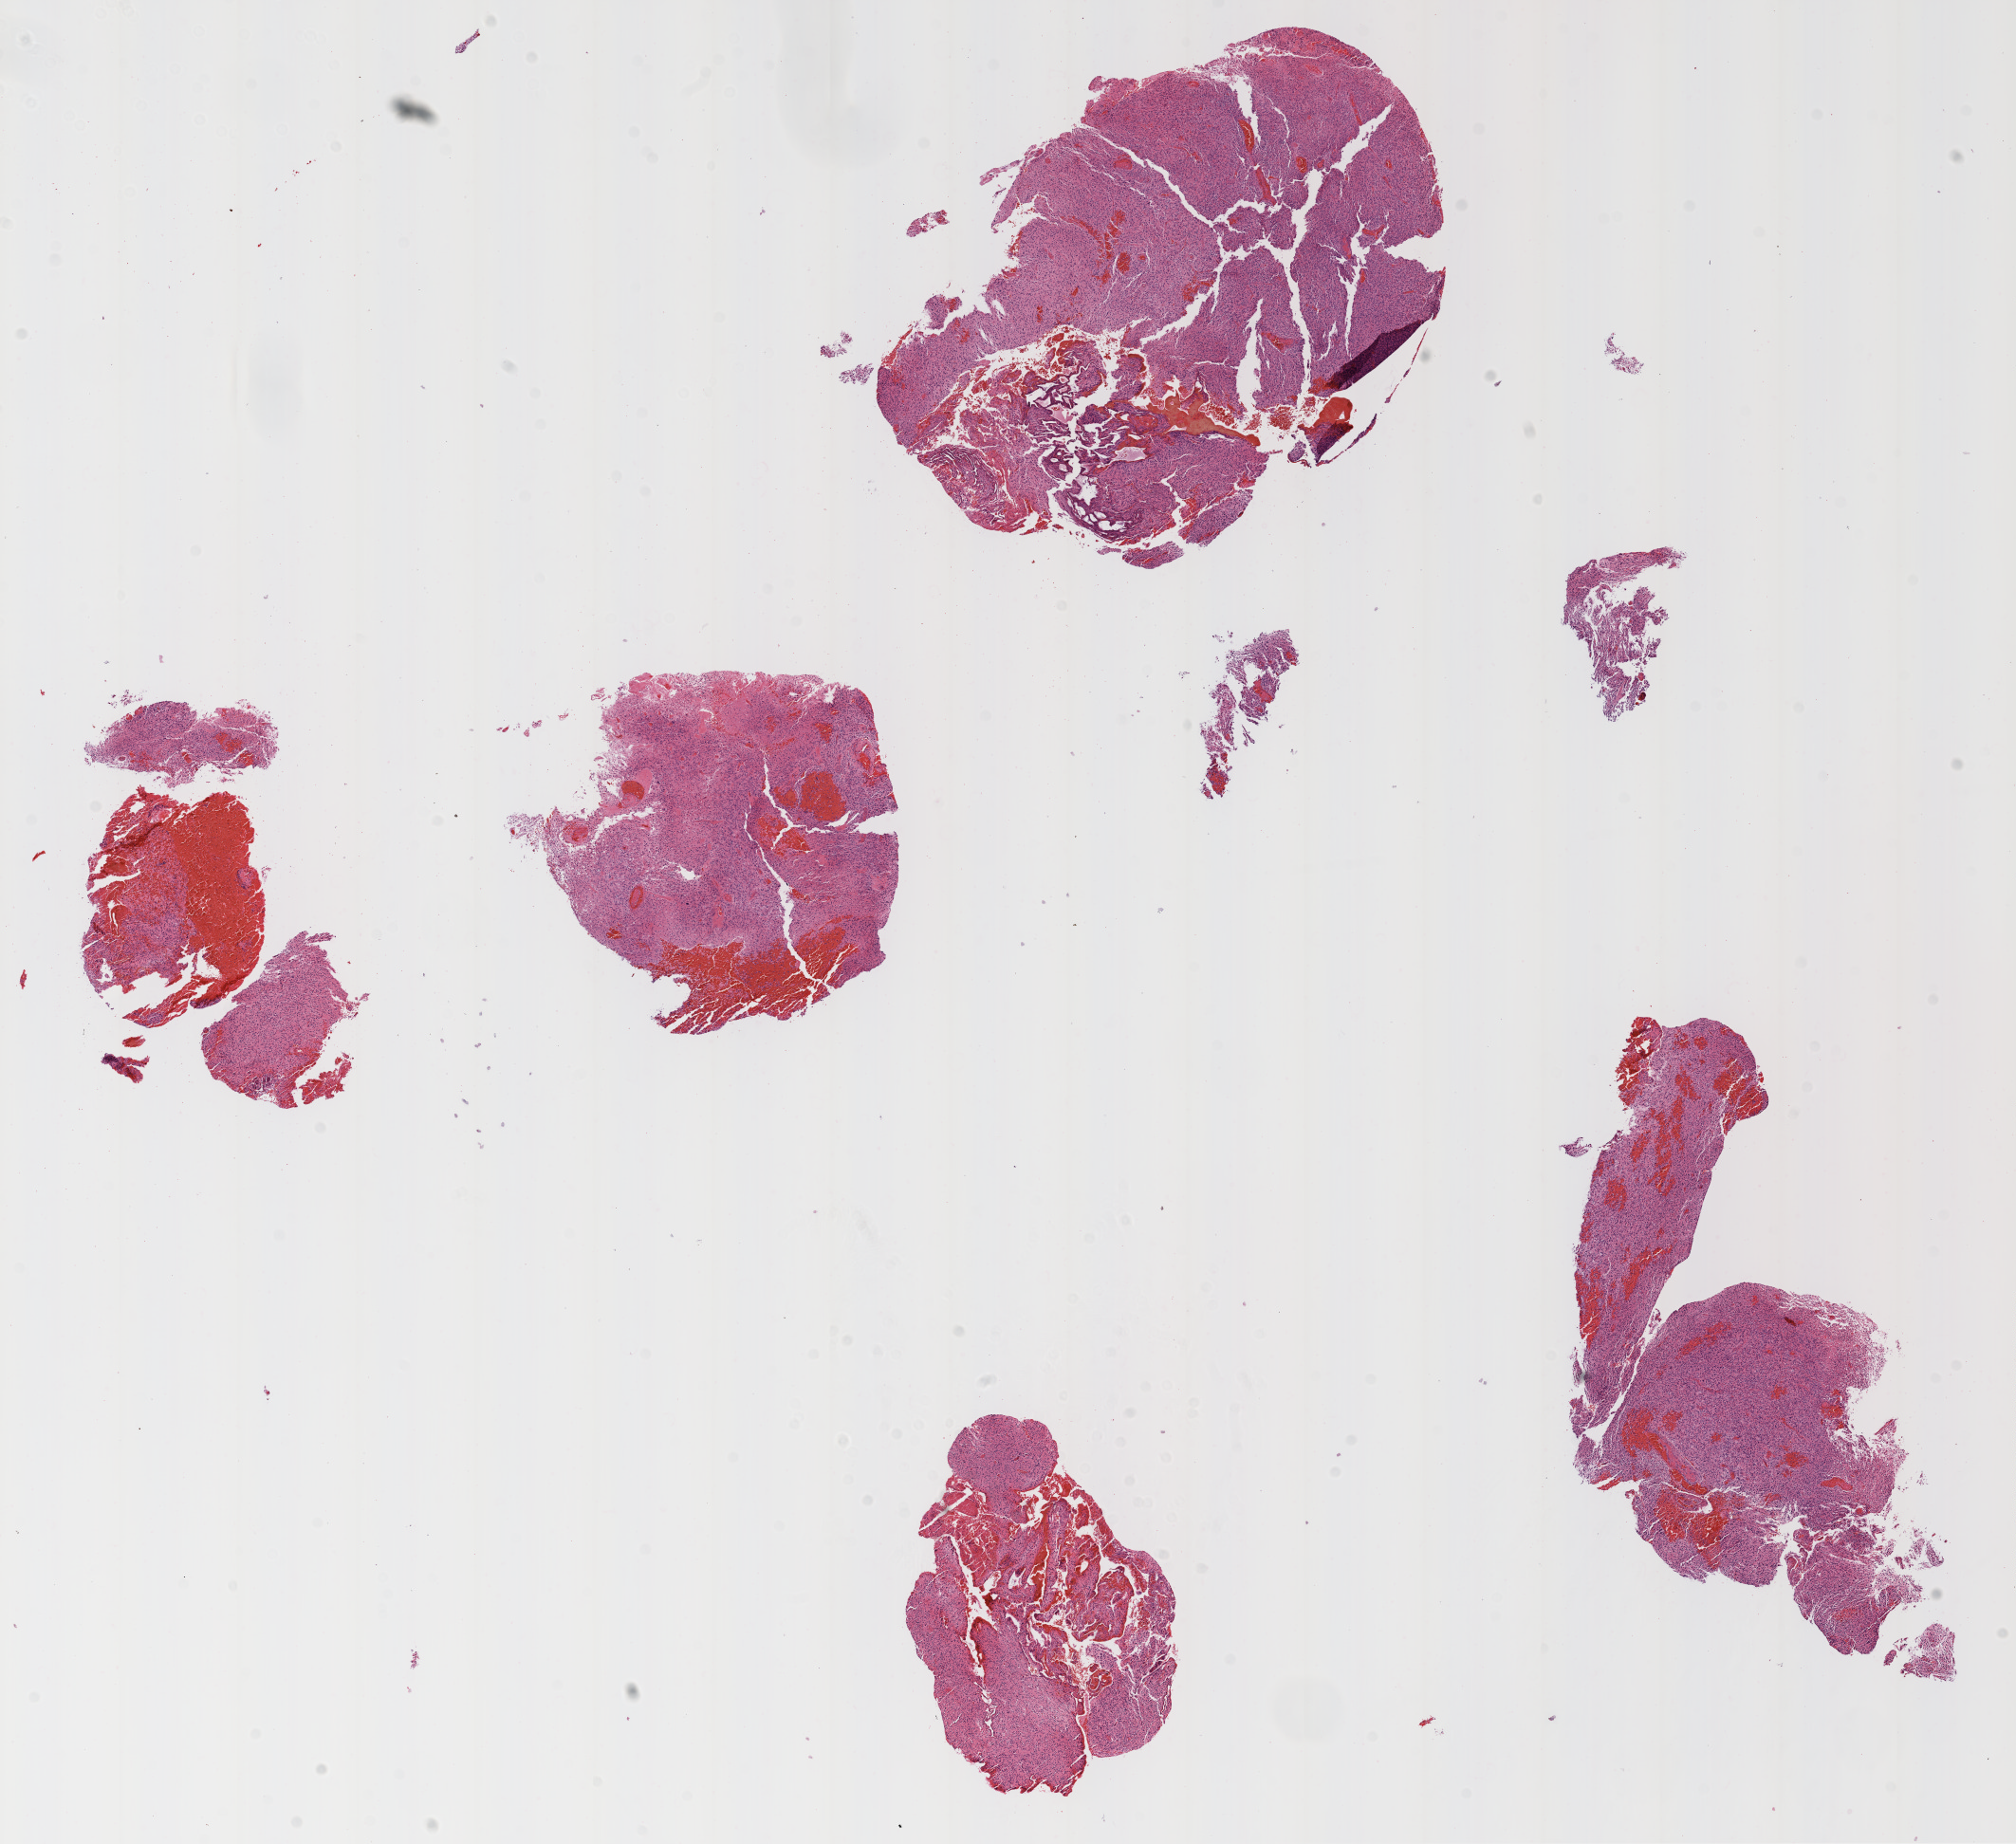
Digitized H&E tissue section (whole slide), low-resolution overview of the scanned area, about 17.1 x 15.6 mm; FFPE section; sample: primary tumour, brain. Patient: male, age at initial diagnosis 67 years.
Pathologic diagnosis: Glioblastoma.